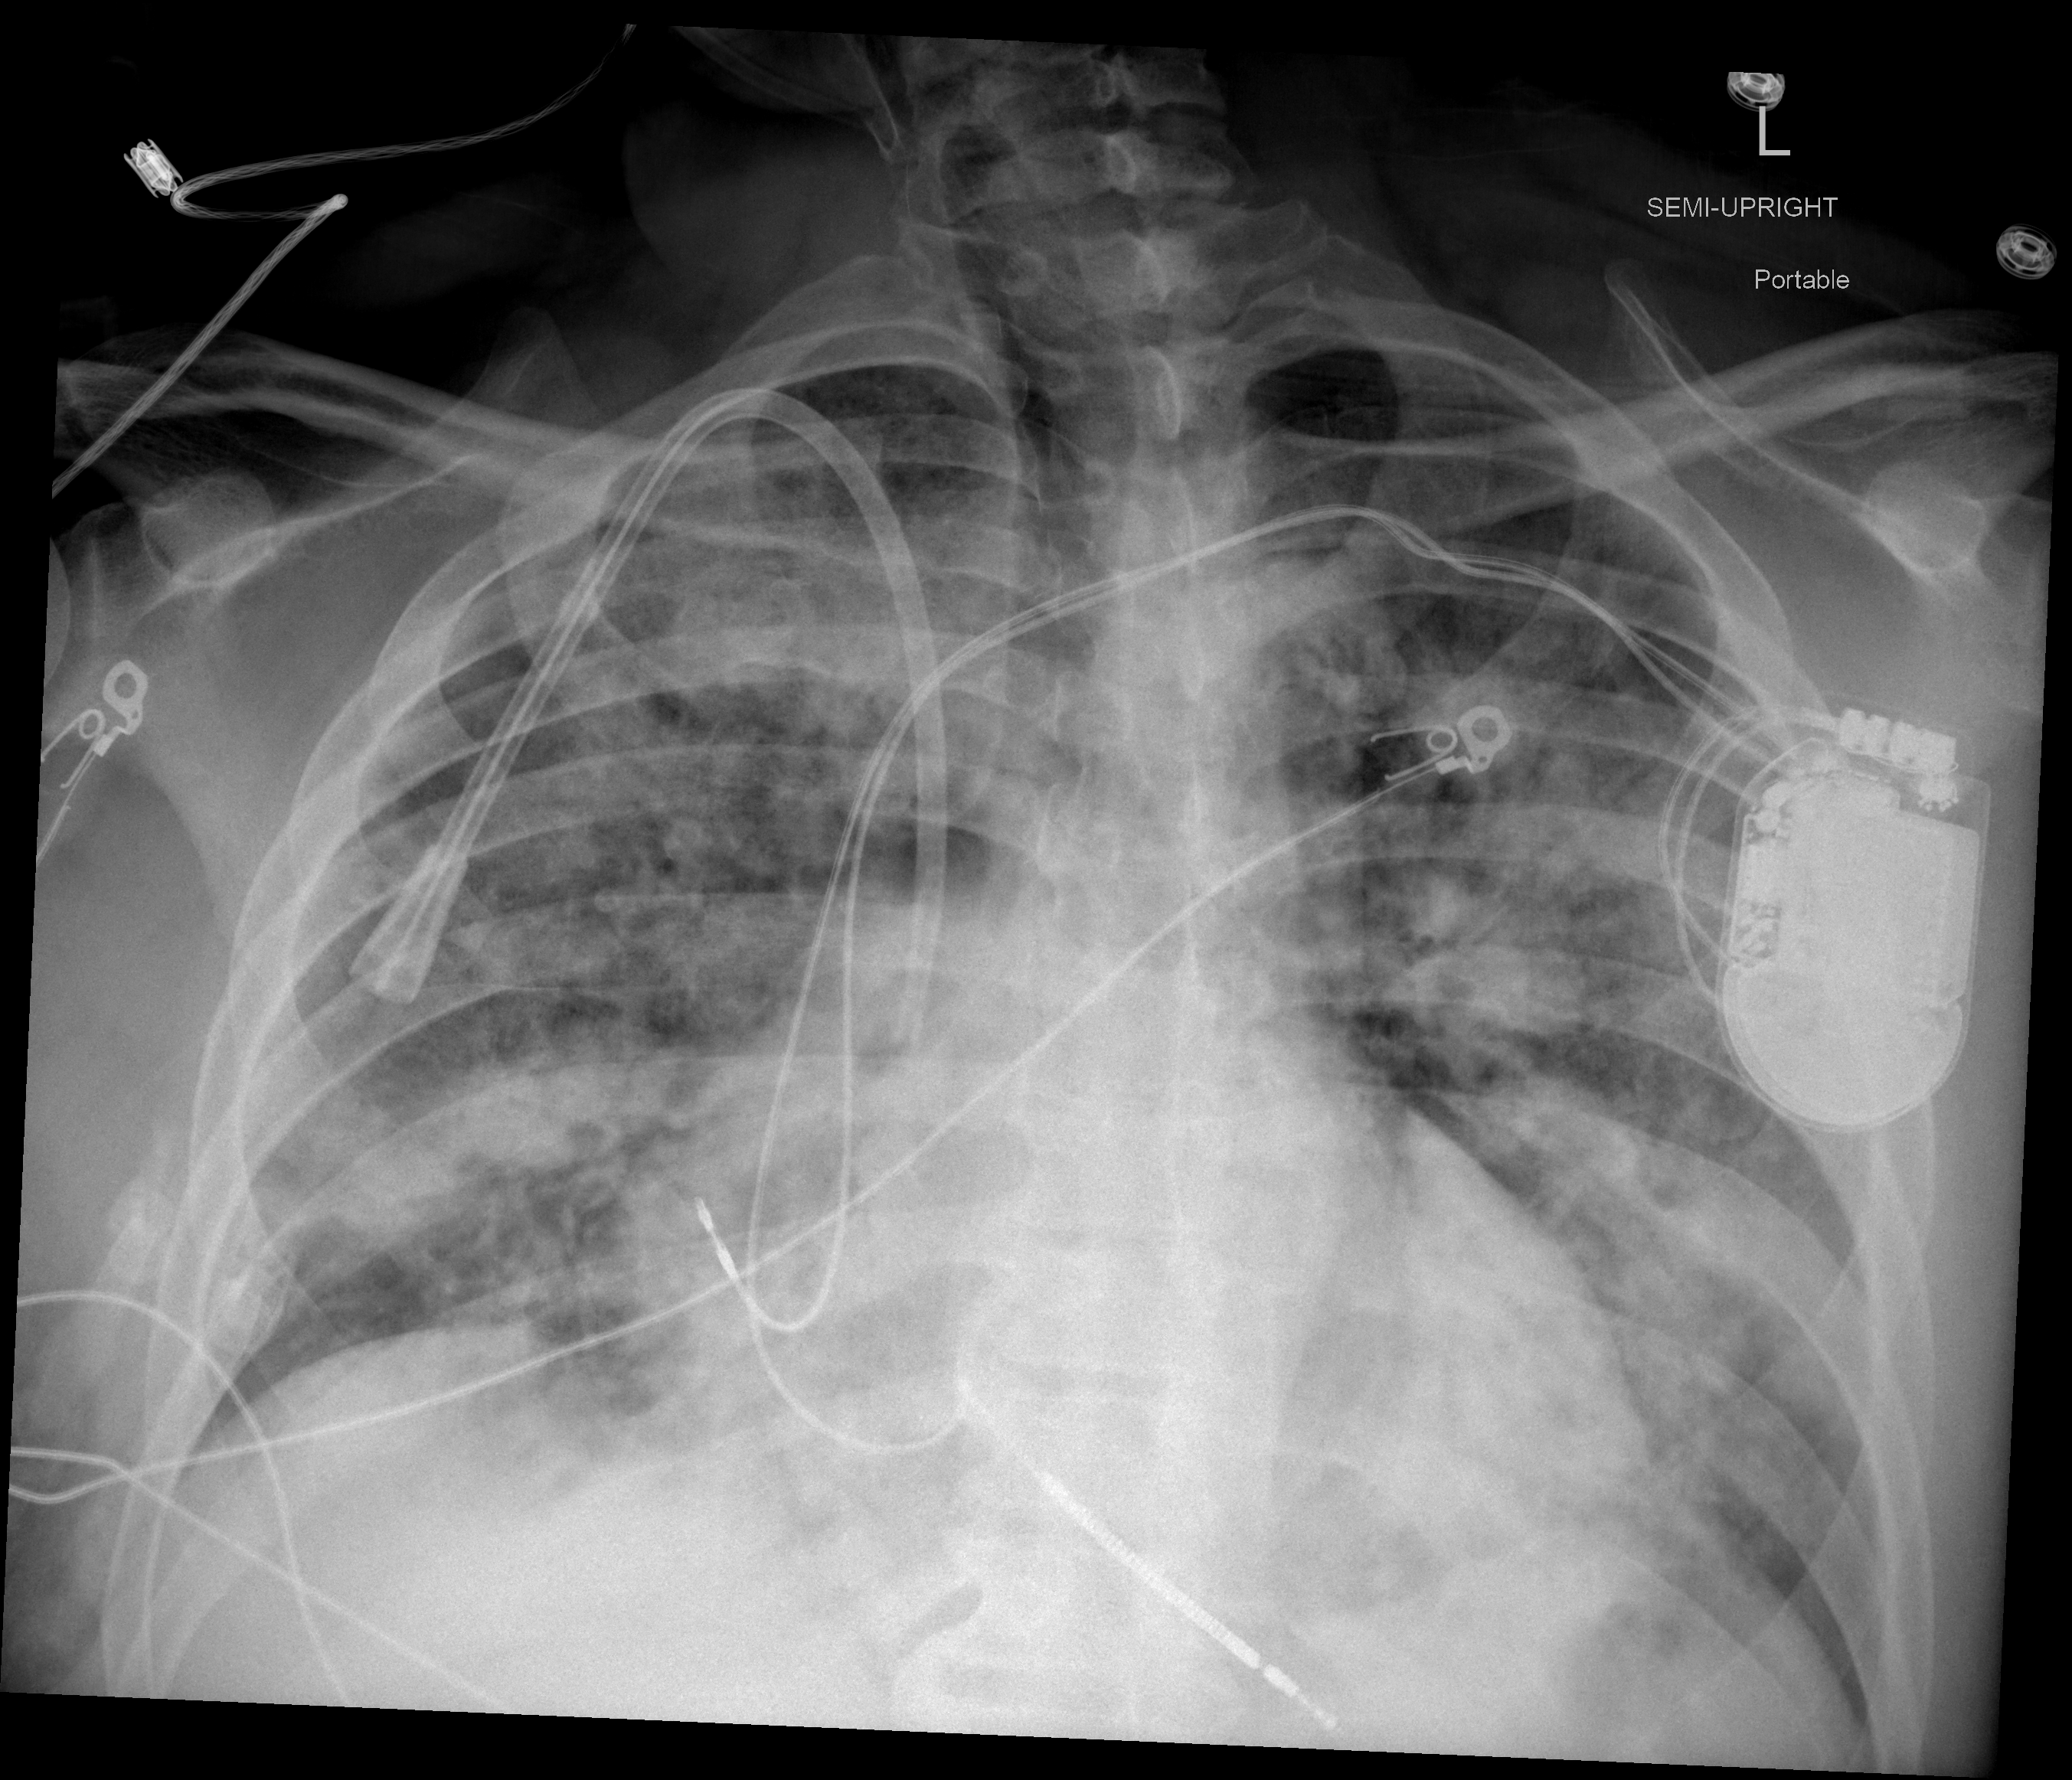
Portable chest radiograph, AP projection. Male patient, age 60 years; COVID-19 (test-positive).
Radiologist's key findings for this exam: Marked interval worsening with now multifocal airspace disease throughout both lungs, somewhat patchy in density and distribution.